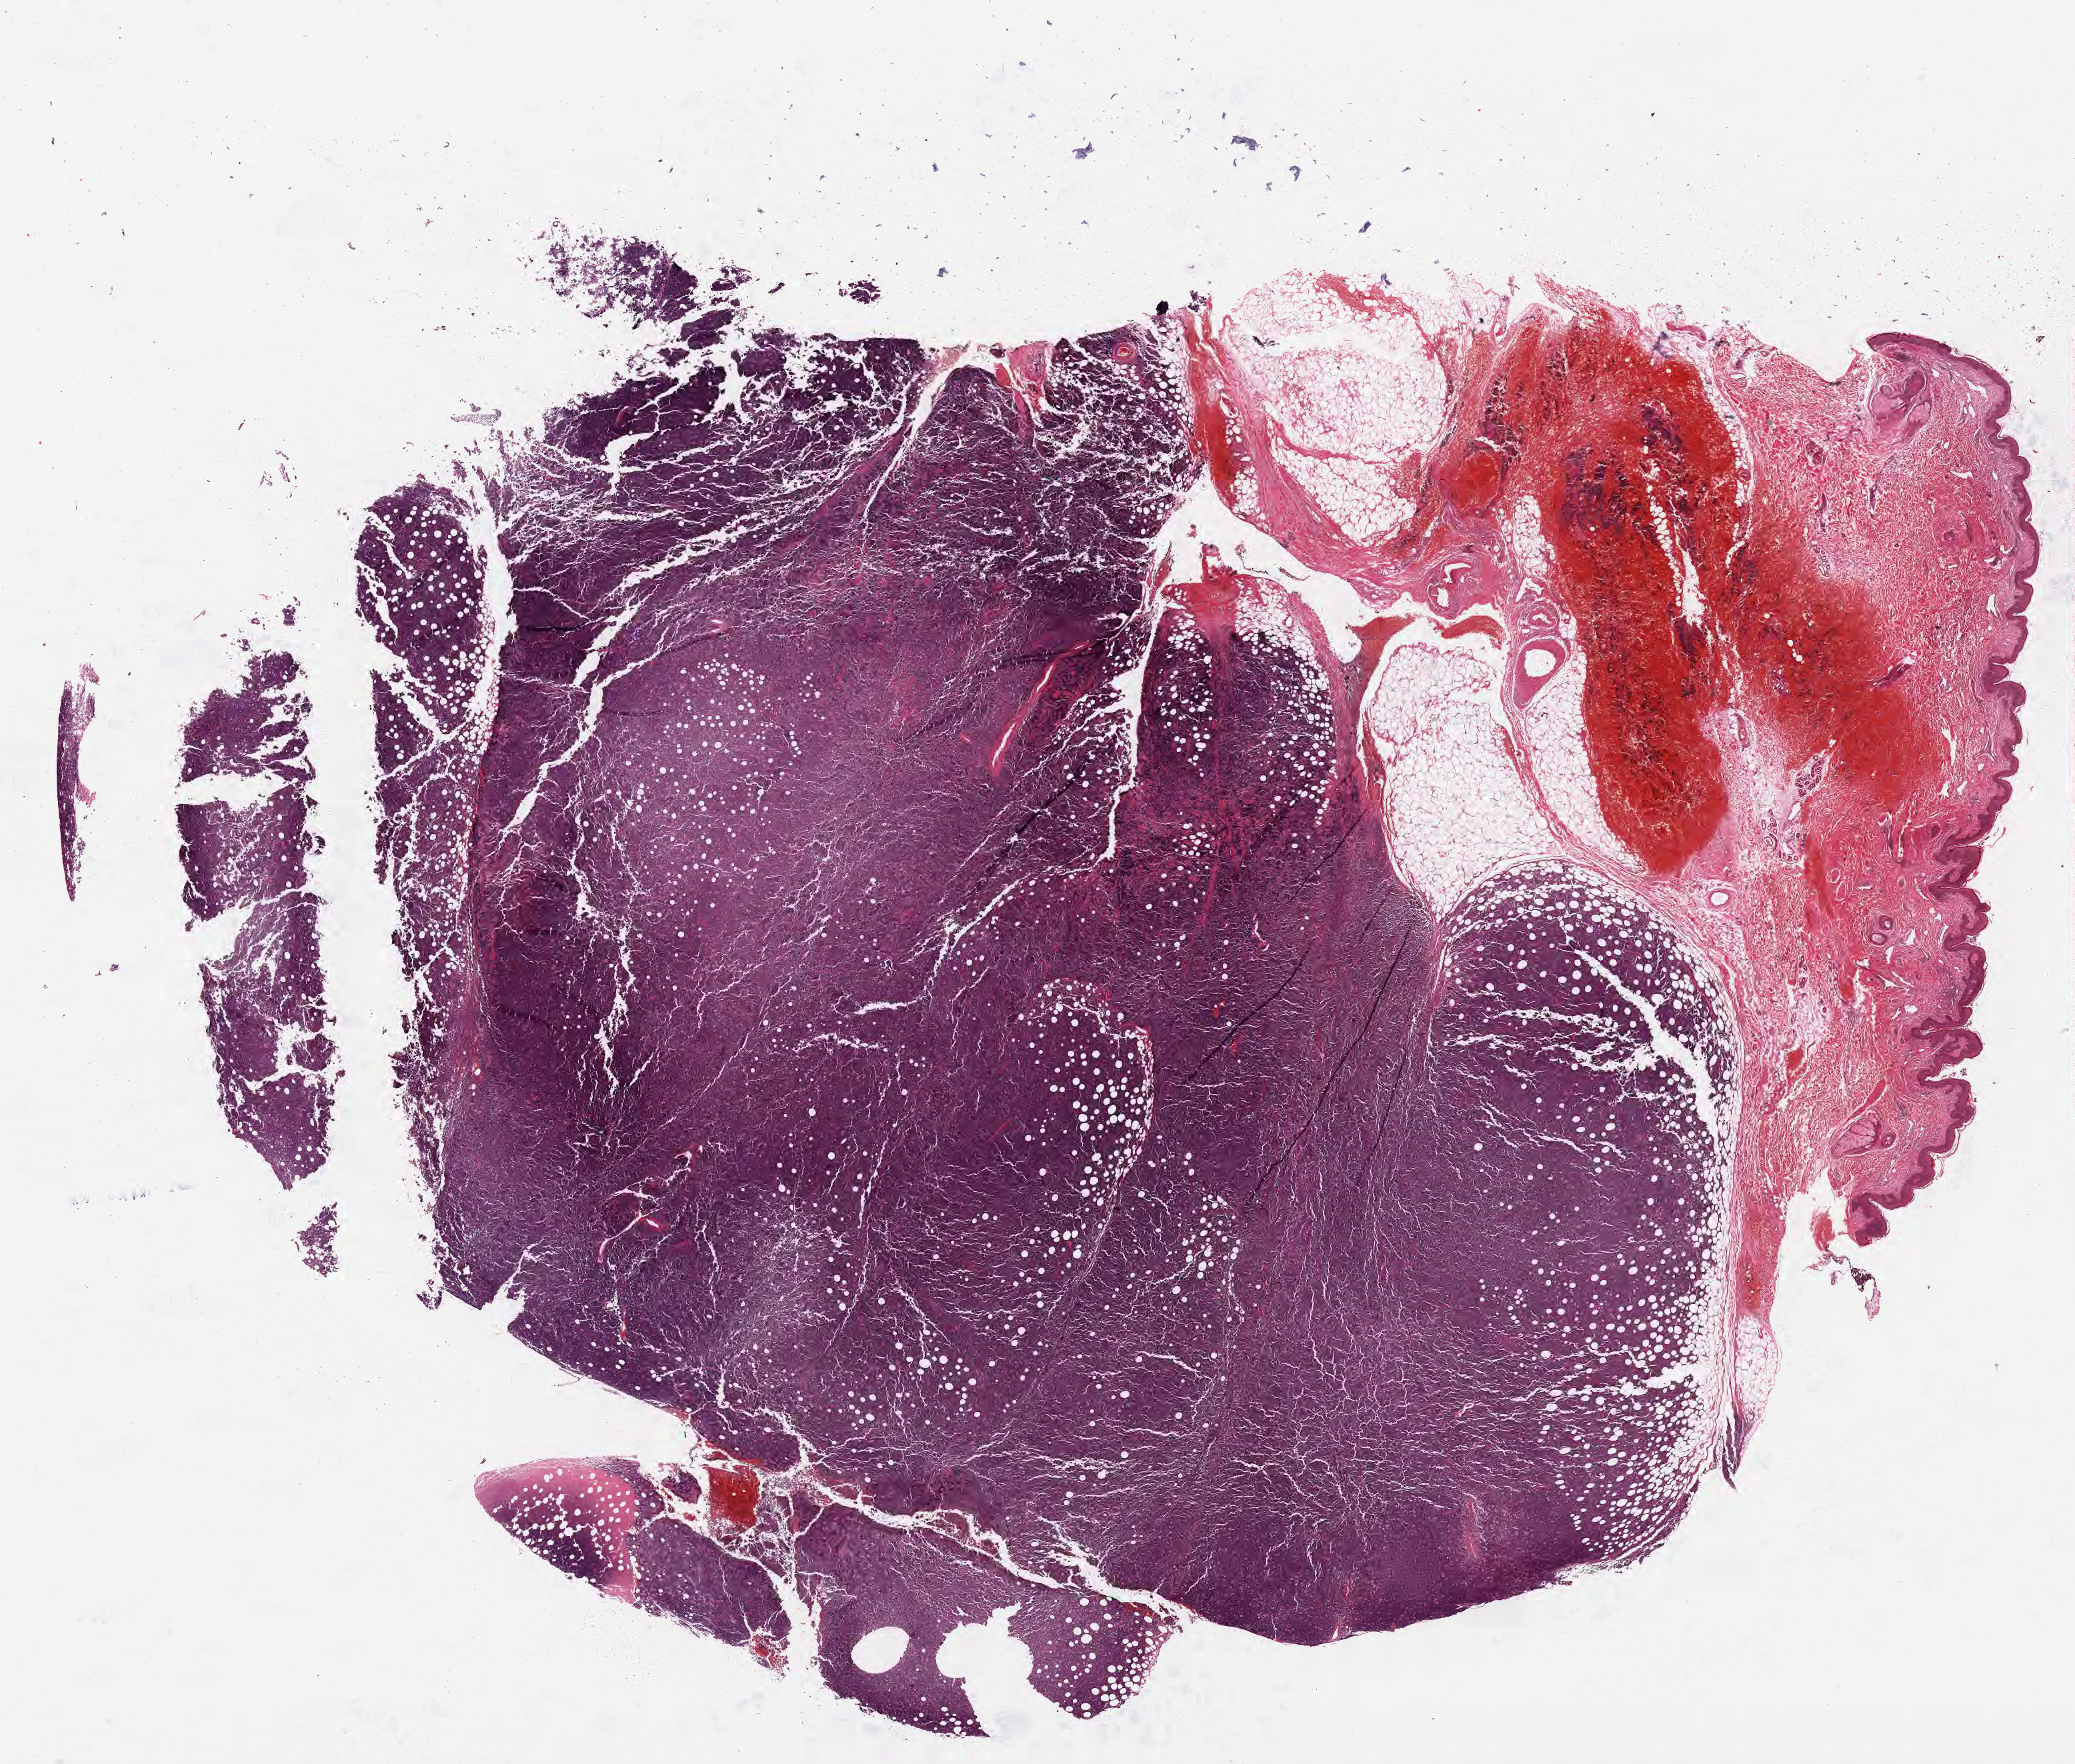
Haematoxylin and eosin whole-slide image, whole scanned area (about 25.1 x 21.4 mm) shown as a low-resolution overview. Formalin-fixed, paraffin-embedded (FFPE) tissue. Primary tumor. Patient: male, age 52 years. Pathologist review of this section (percent, as recorded): tumor cells 85%, tumor nuclei 90%, stromal cells 10%, necrosis 0%, normal cells 5%. Infiltration values recorded for this section: lymphocyte infiltration 70%, monocyte infiltration 20%, neutrophil infiltration 5%.
Ann Arbor stage (patient): Stage IV. Section: bottom of the tissue portion. Histologic diagnosis: Burkitt lymphoma, NOS.